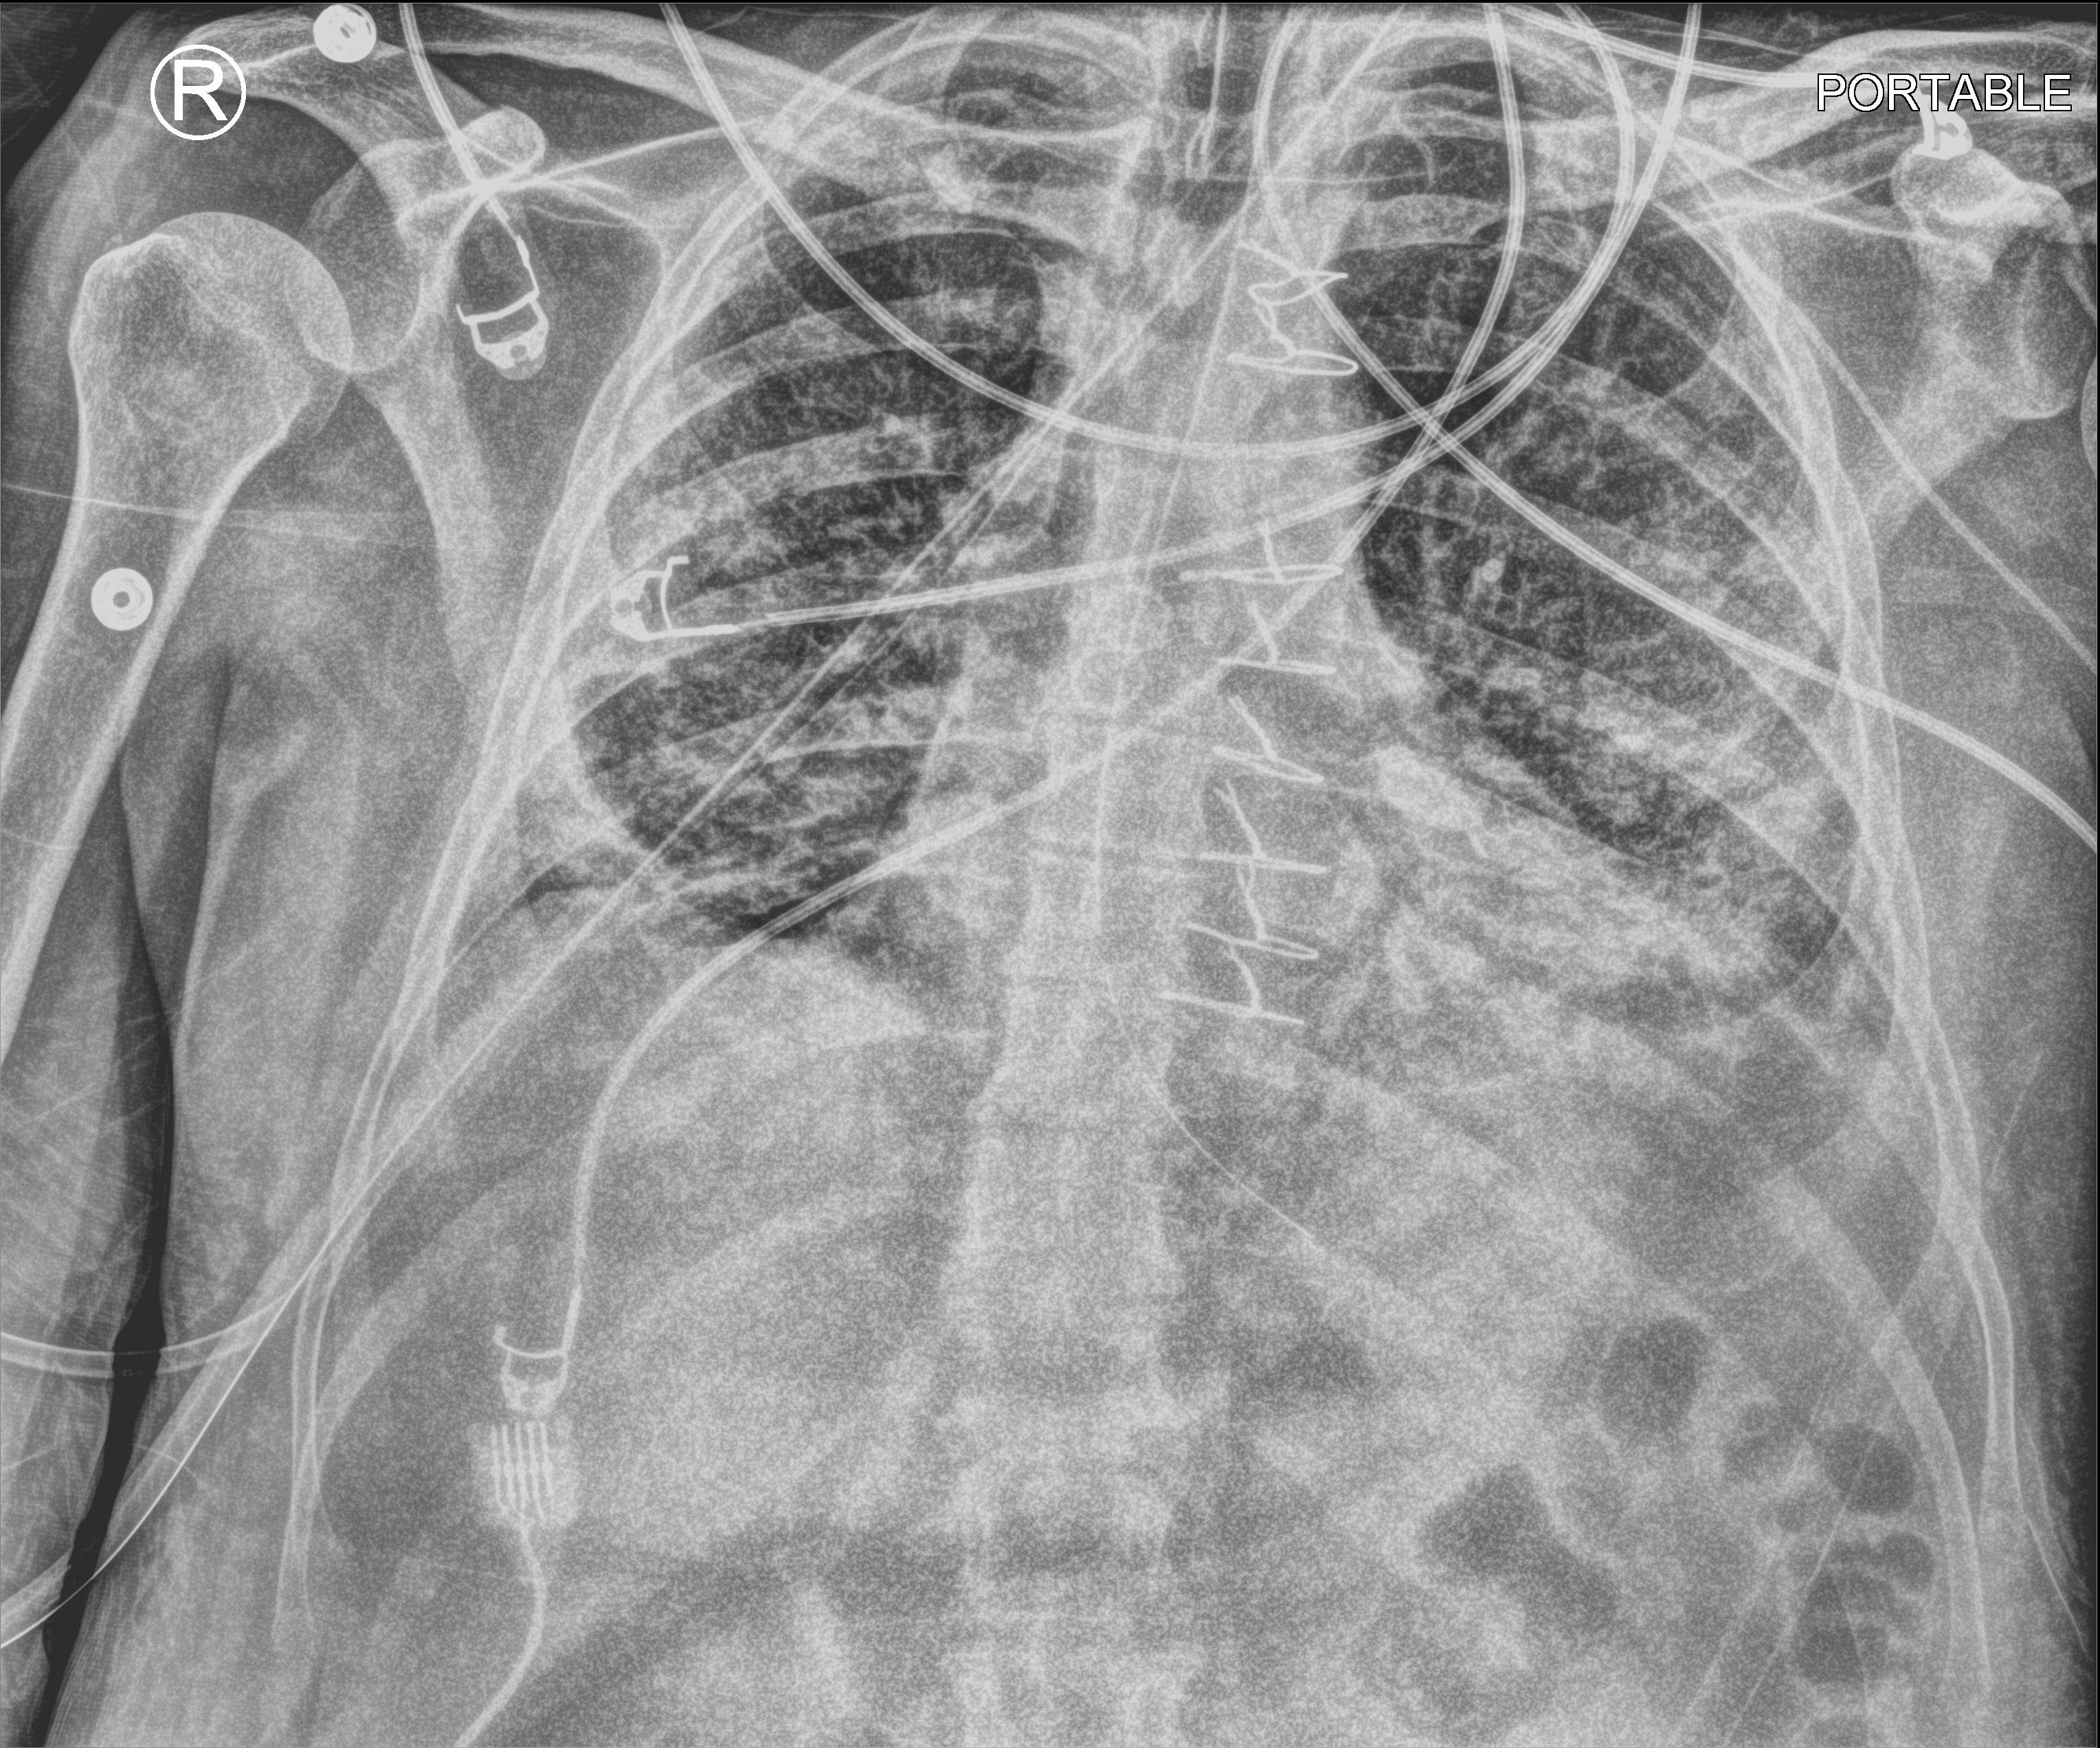
Portable chest radiograph, anteroposterior (AP) projection. Patient hospitalised with COVID-19; male, aged 18–59 years.
Admission-level facts for this patient (not findings on this image; timing relative to this image not recorded): mechanically ventilated during this hospital stay: yes; admitted to intensive care during this hospital stay: yes; hypertension (admission record): no.